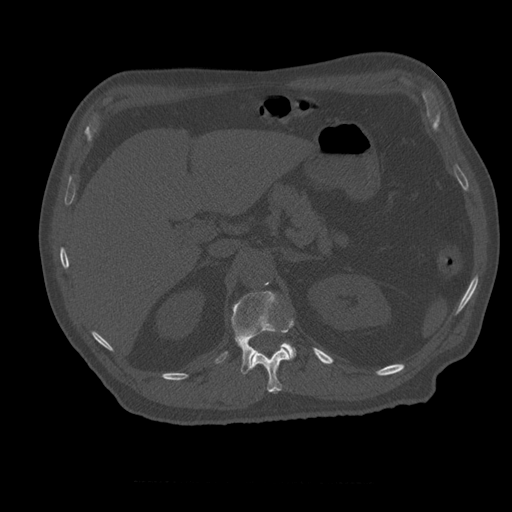
CT including the spine, one axial slice; position 250 of 399 along the scan axis; reconstruction kernel STANDARD; bone window (W 1800 / L 400 HU); 1.25 mm slice thickness; 512 × 512 image matrix, field of view 407 × 407 mm. Patient age 73 years. Case-level facts recorded for this patient, not image findings: primary cancer: prostate.
Outlined on this slice (semi-automatic segmentation, software-assisted and operator-edited):
- L1 vertebra: box from (x=215, y=291) to (x=296, y=375) px
- T12 vertebra: (x=251, y=320)–(x=294, y=394)